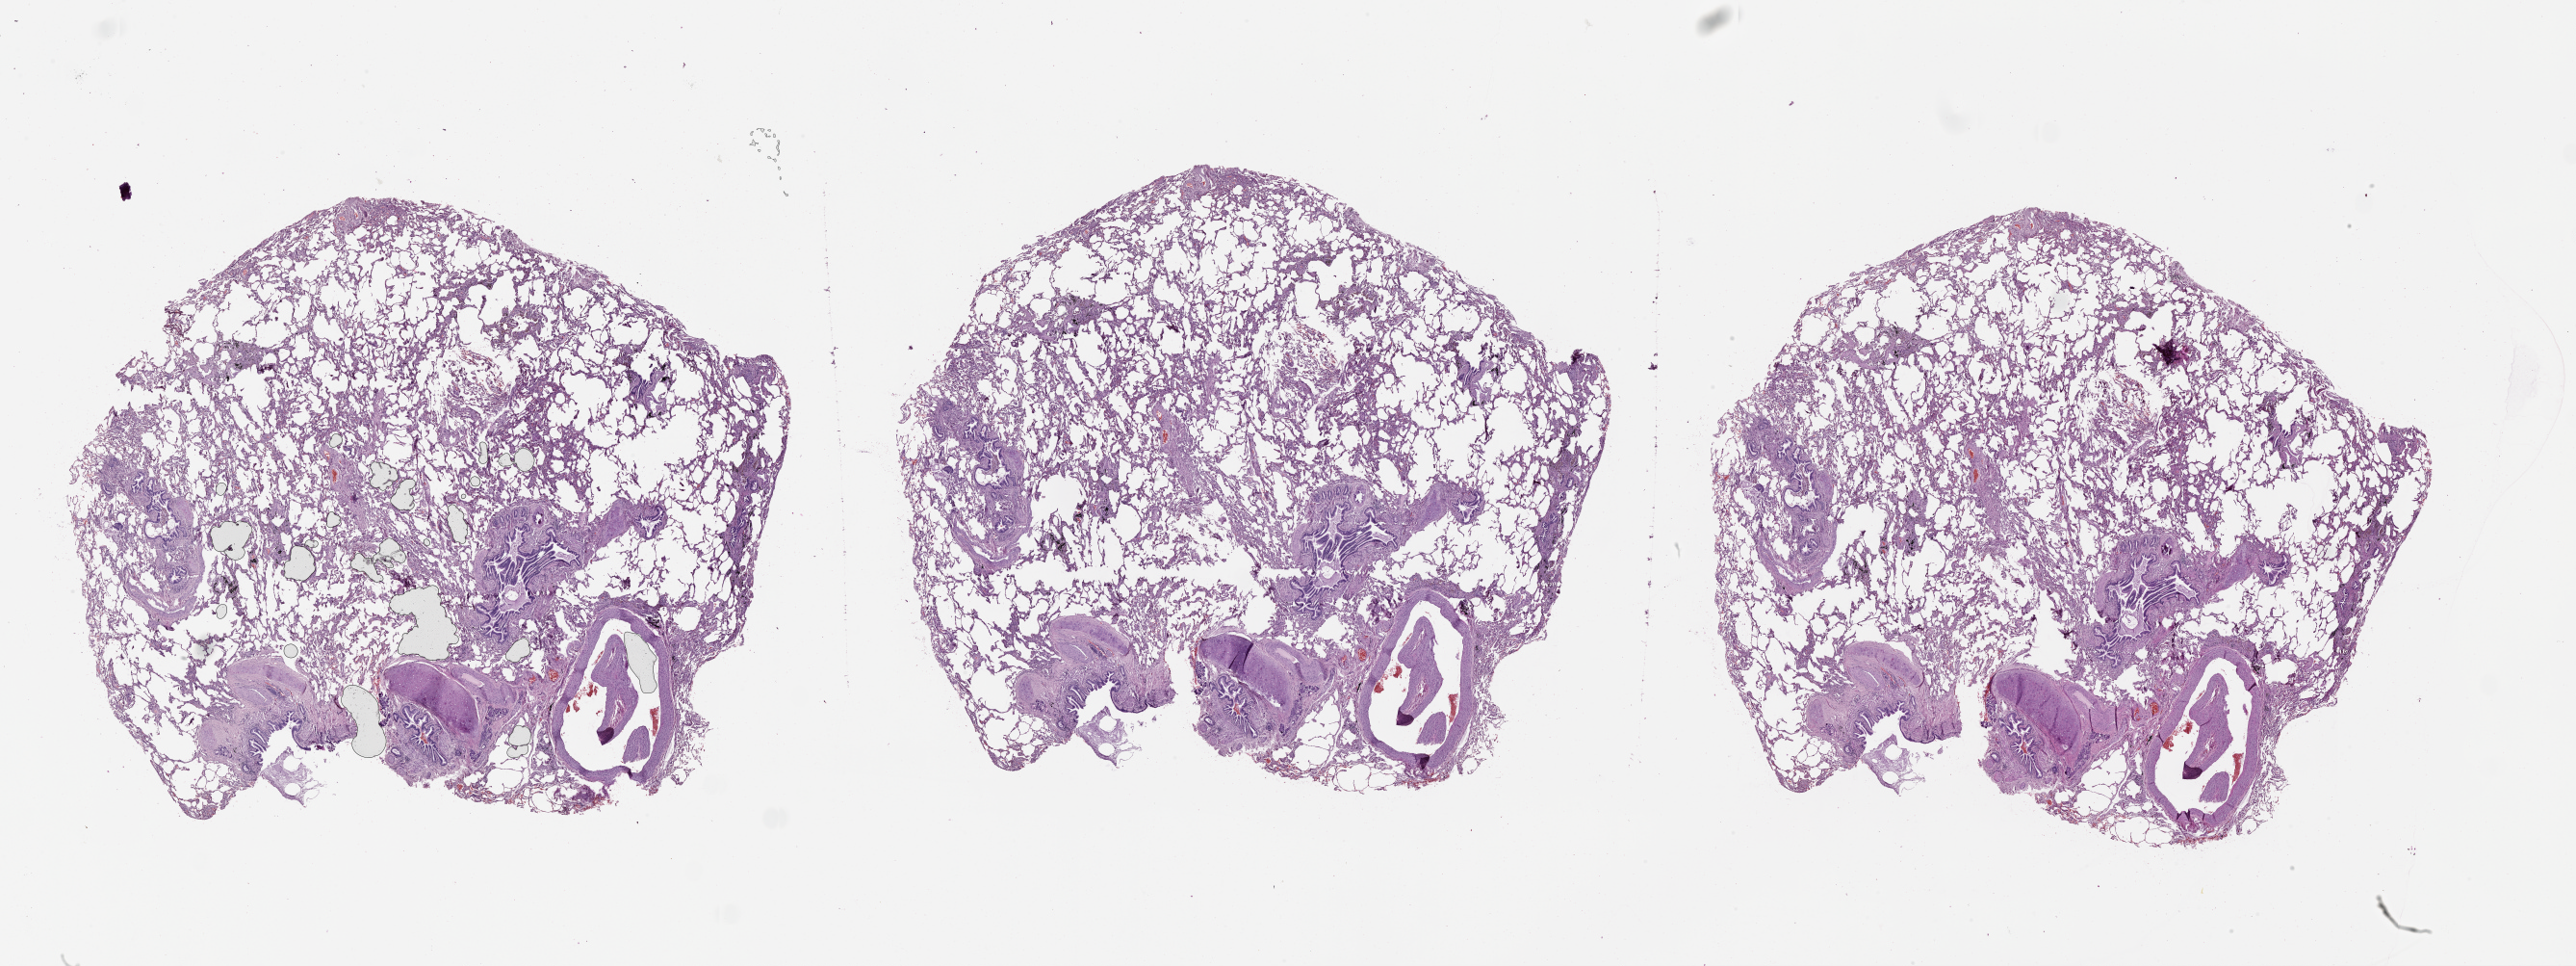
Digitized H&E tissue section (whole slide), a low-resolution overview of the entire scanned area, about 43.1 x 16.2 mm (from a 20x scan). Lung, normal (non-tumour) tissue. Patient: female, age 62 years.
- this section: normal (non-tumour) tissue from the same patient
- patient diagnosis (cohort enrolment): squamous cell carcinoma (lung)